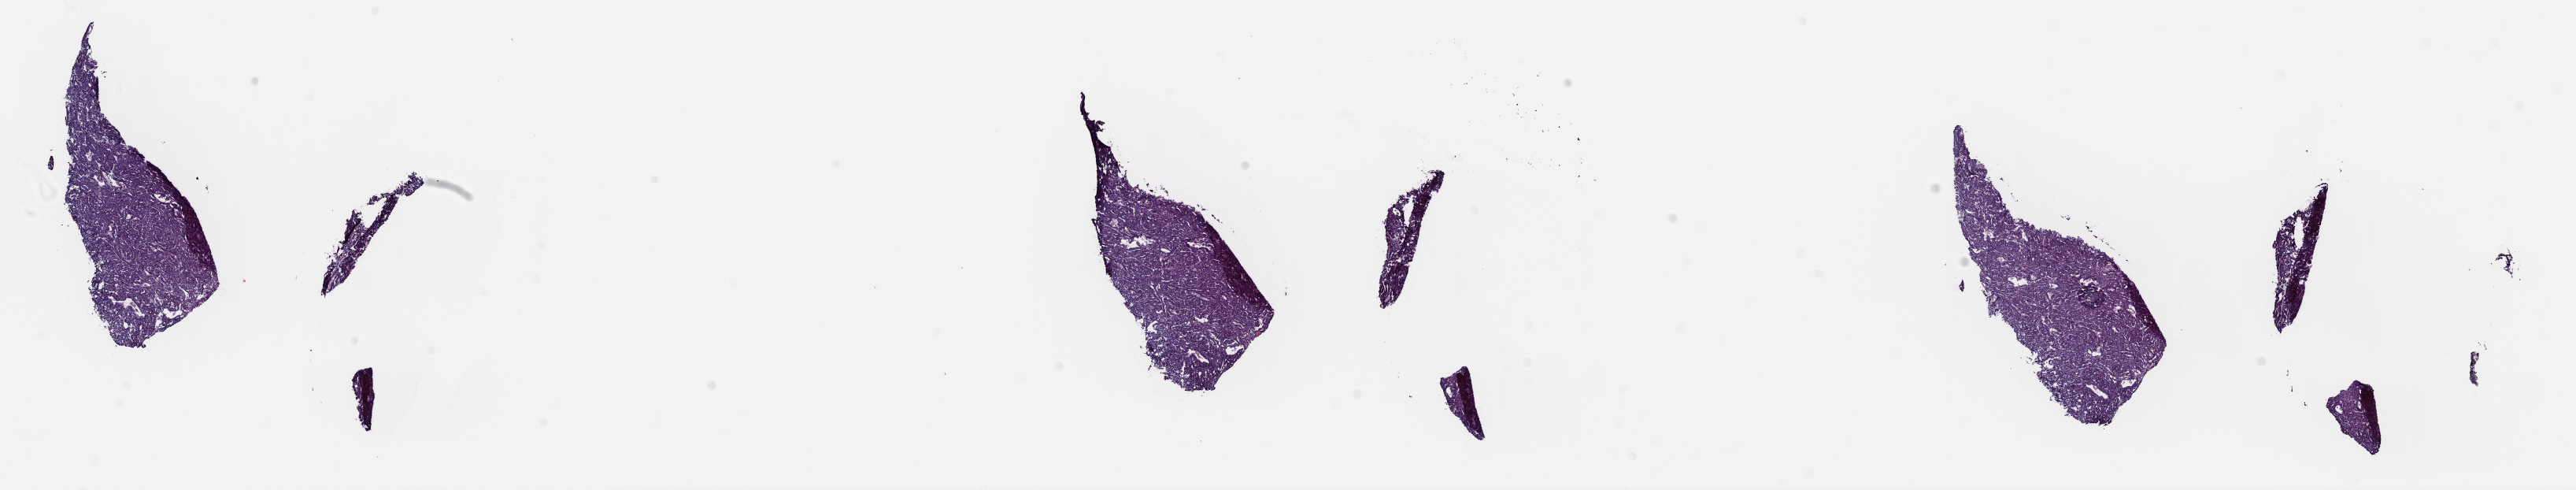
Whole-slide histology image, Hematoxylin and eosin (H&E) stained, low-resolution overview of the scanned area, about 25.8 x 4.9 mm, frozen section from the top of the tissue portion, sample: primary tumour, ovary. Female patient; age at initial diagnosis 78 years. Histologic grade: G3 (poorly differentiated). Composition of this section per pathologist review: tumour cells 100%, tumour nuclei 85%, normal cells 0%, stromal cells 0%, necrosis 0%. Inflammatory infiltration, as recorded: lymphocyte infiltration 1%, monocyte infiltration 0%, neutrophil infiltration 0%.
Laterality: left. Pathologic diagnosis: Serous cystadenocarcinoma, NOS. FIGO stage: IIA.